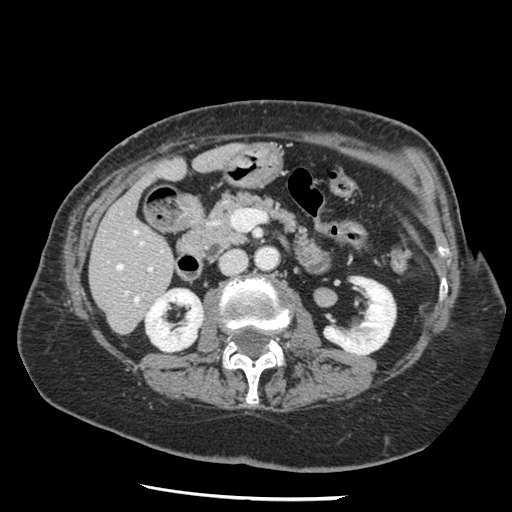
Contrast-enhanced abdominal CT, one axial slice; slice 54 of 148 in the series (ordered by position); reconstruction kernel STANDARD; intravenous contrast given; soft-tissue window (W 400 / L 40 HU); 2.5 mm slice thickness; 512 × 512 image matrix. Female patient, age 85 years. Case-level facts recorded for this patient, not image findings: diagnosis: colorectal cancer liver metastases, imaged before liver resection.
Structures marked on this image (expert manual segmentation):
- hepatic veins: bounding box [x1, y1, x2, y2] px = [116, 231, 138, 302]
- liver: [91, 146, 237, 333]
- planned liver remnant (the part of the liver to remain after resection): [94, 146, 237, 326]